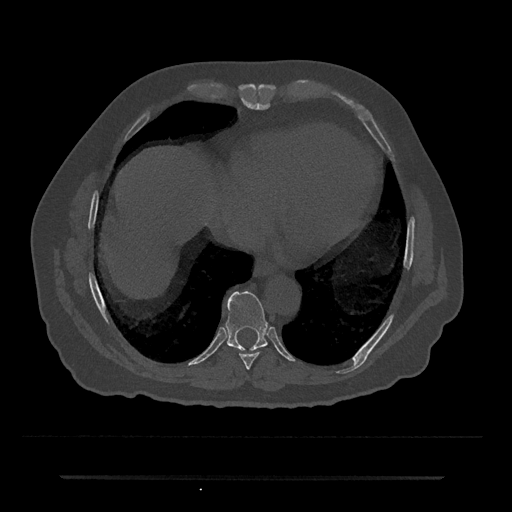
CT including the spine, one axial slice. Slice 301 of 797 in the series (ordered by position). Bone window (W 1800 / L 400 HU). 512 × 512 image matrix, field of view 437 × 437 mm. Patient: male, 69 years. From the clinical record (not read from this slice): primary cancer: prostate.
Structures marked on this image (semi-automatically segmented with operator editing):
- T8 vertebra: bounding box [x1, y1, x2, y2] px = [240, 349, 260, 369]
- T9 vertebra: [225, 291, 268, 351]